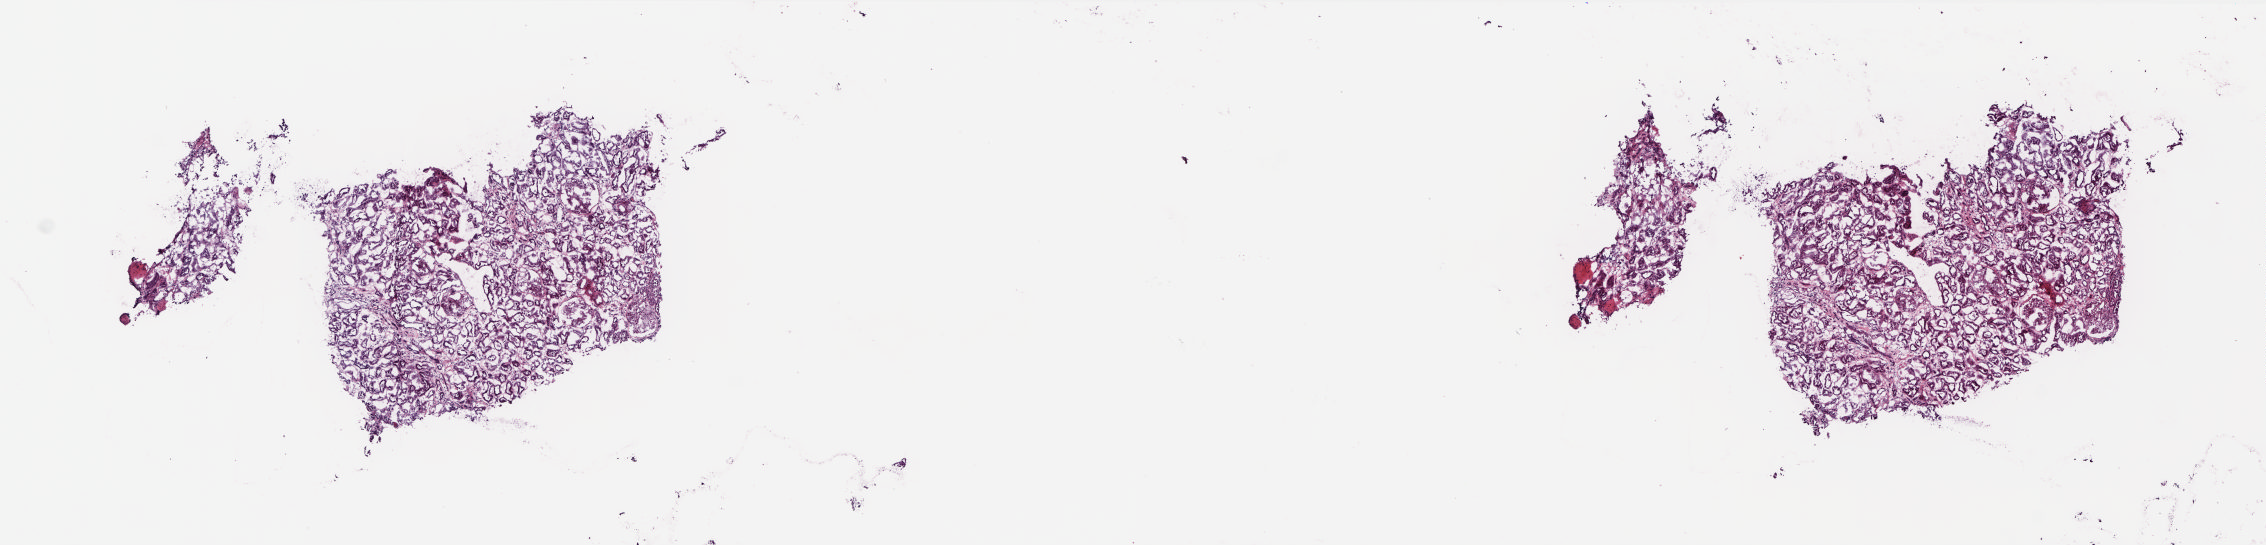
Digitized H&E-stained tissue section (whole slide) — low-resolution overview of the scanned area, about 18.3 x 4.4 mm (slide scanned at 20x), frozen section from the top of the tissue portion, solid tissue normal (non-tumour tissue) sample from the kidney. Female, age 57 years at initial diagnosis. Slide review estimates, as recorded: tumour cells 0%, tumour nuclei 0%, normal cells 70%, stromal cells 30%, necrosis 0%. Infiltration values recorded for this section: lymphocyte infiltration 5%, monocyte infiltration 0%, neutrophil infiltration 0%.
This section: solid tissue normal sample (biorepository sample class). Patient diagnosis: Renal cell carcinoma, NOS.